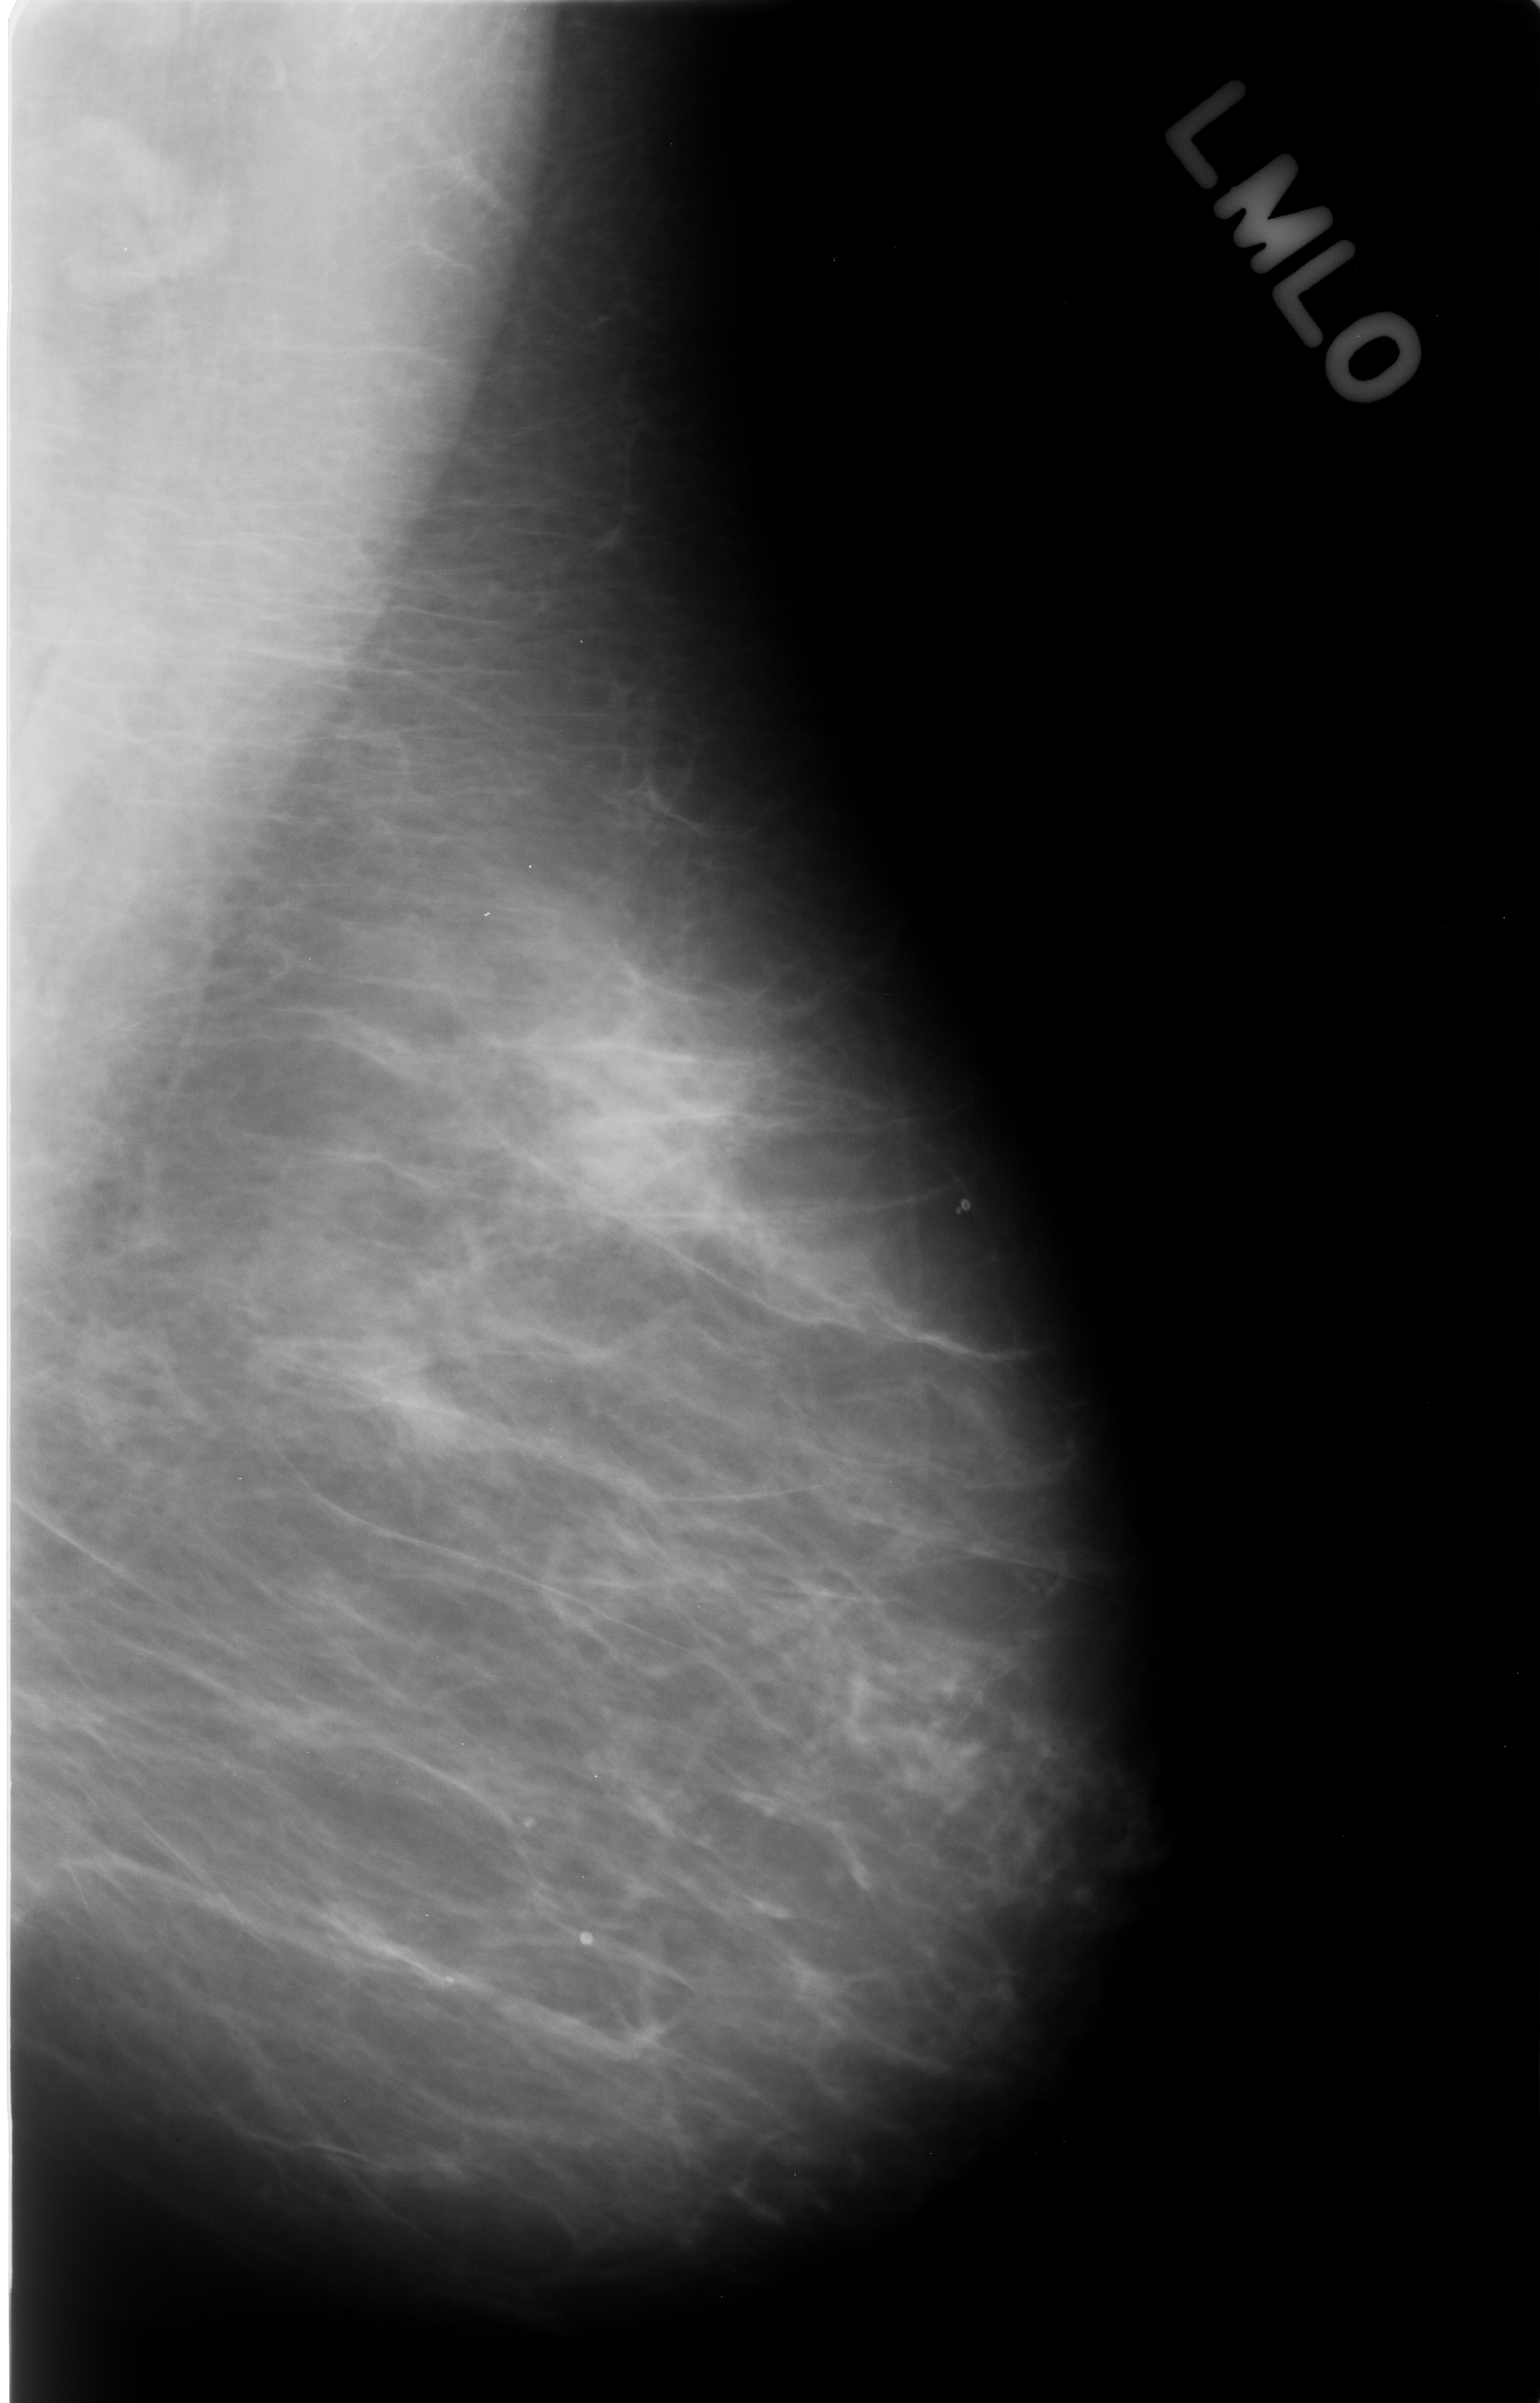
Scanned film-screen mammogram; left breast; mediolateral oblique (MLO) view; 1540 × 2403 image matrix.
Expert-marked regions of interest on this film, with their recorded descriptors:
- mass, shape oval, margins circumscribed; BI-RADS assessment category 3; subtlety rating 3 on a 1 (subtle) to 5 (obvious) scale; outcome (as recorded, no biopsy): benign without callback (not worked up further): bounding box <335,1332,479,1466> (left, top, right, bottom; pixels)